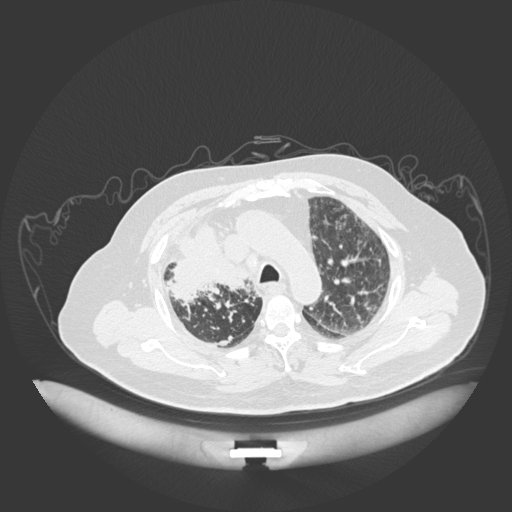
Chest CT, one axial slice; slice 136 of 201 in the series (ordered by position); 120 kVp; lung window (W 1500 / L -600 HU); 1 mm slice thickness; 512 × 512 image matrix, field of view 500 × 500 mm. Patient: male, 69 years. Case-level facts recorded for this patient, not image findings: clinical TNM (as recorded): T4 N3 M1.
Outlined on this slice (bounding box drawn by a radiologist):
- lung tumour (recorded histology: adenocarcinoma): box from (x=167, y=224) to (x=251, y=305) px